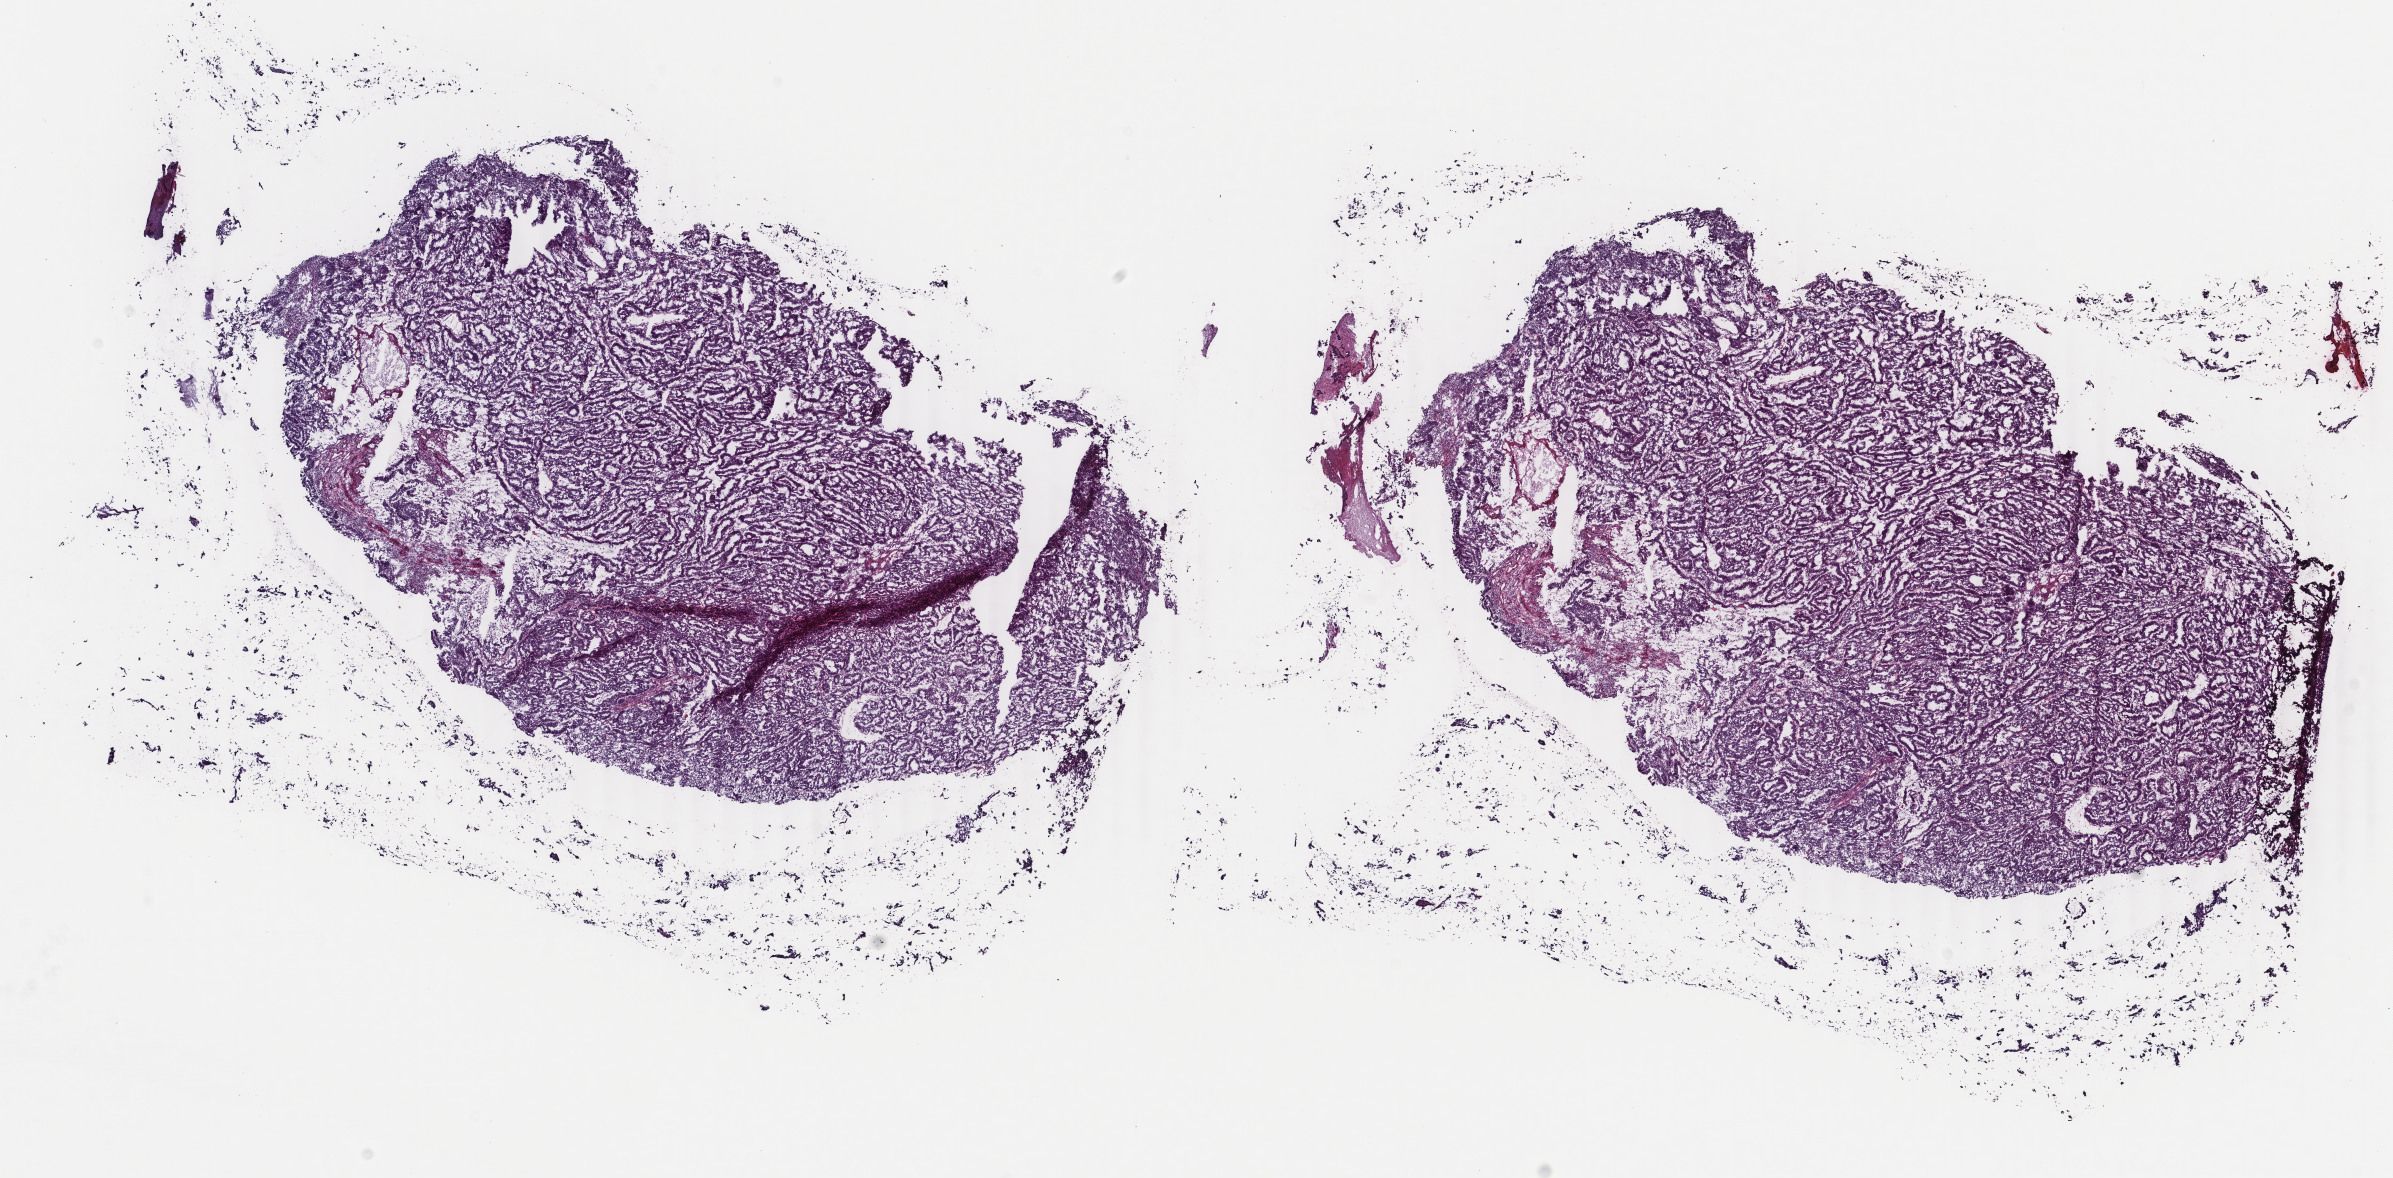
Whole-slide histology image, H&E-stained — shown as a low-resolution overview of the whole scanned area (about 19.0 x 9.4 mm, slide scanned at 40x). Frozen section. Uterus, primary tumour sample. Patient: female, age at initial diagnosis 55 years. Histologic grade: G2 (moderately differentiated). Pathologist review of this section (percent, as recorded): tumour cells 90%, tumour nuclei 90%, normal cells 0%, stromal cells 5%, necrosis 5%. Infiltration values recorded for this section: lymphocyte infiltration 3%, monocyte infiltration 6%, neutrophil infiltration 1%.
Lymph nodes positive (case pathology): 0 of 13 examined. Pathologic diagnosis: Endometrioid adenocarcinoma, NOS. FIGO stage: IA.